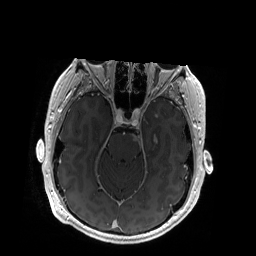
Brain MRI from a brain-tumour surgery series, one axial slice. T1-weighted post-contrast. 1 mm slice thickness. 256 × 256 image matrix. From the clinical record (not read from this slice): histopathology: Glioblastoma; WHO grade: 4; IDH mutation: no.
Outlined on this slice (outlined manually by an expert reader):
- tumour: box from (x=133, y=135) to (x=158, y=144) px